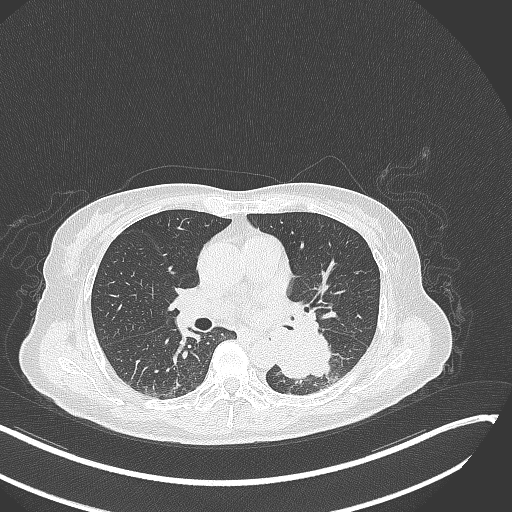
Chest CT, one axial slice. Slice 148 of 342 in the series (ordered by position). 120 kVp. Lung window (W 1500 / L -600 HU). 1 mm slice thickness. 512 × 512 image matrix. Female patient, age 64 years. Case-level facts recorded for this patient, not image findings: clinical TNM (as recorded): T3 N1 M1; histopathological grade: G3.
Structures marked on this image (bounding box drawn by a radiologist):
- lung tumour (recorded histology: small cell carcinoma): bounding box (x1, y1, x2, y2) in pixels: (268, 325, 333, 380)